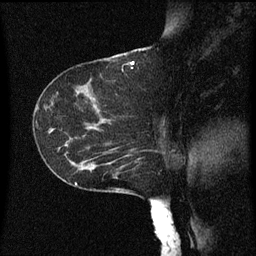
Breast MRI (dynamic contrast-enhanced), one sagittal slice. Dynamic contrast-enhanced series, image 2 of 3 at this slice position (ordered by acquisition). 1.5 T. TE 4.2 ms, TR 8 ms. 2 mm slice thickness. 256 × 256 image matrix. Female patient, age 55 years.
Annotated regions visible in this slice (semi-automatically segmented with operator editing):
- analysis volume of interest (the breast-tissue region the enhancement analysis was run in; not a lesion): bounding box (x1, y1, x2, y2) in pixels: (46, 124, 149, 181)
- tumour enhancement mask (voxels above the 70 % enhancement threshold inside the analysis volume of interest): (78, 154, 131, 171)